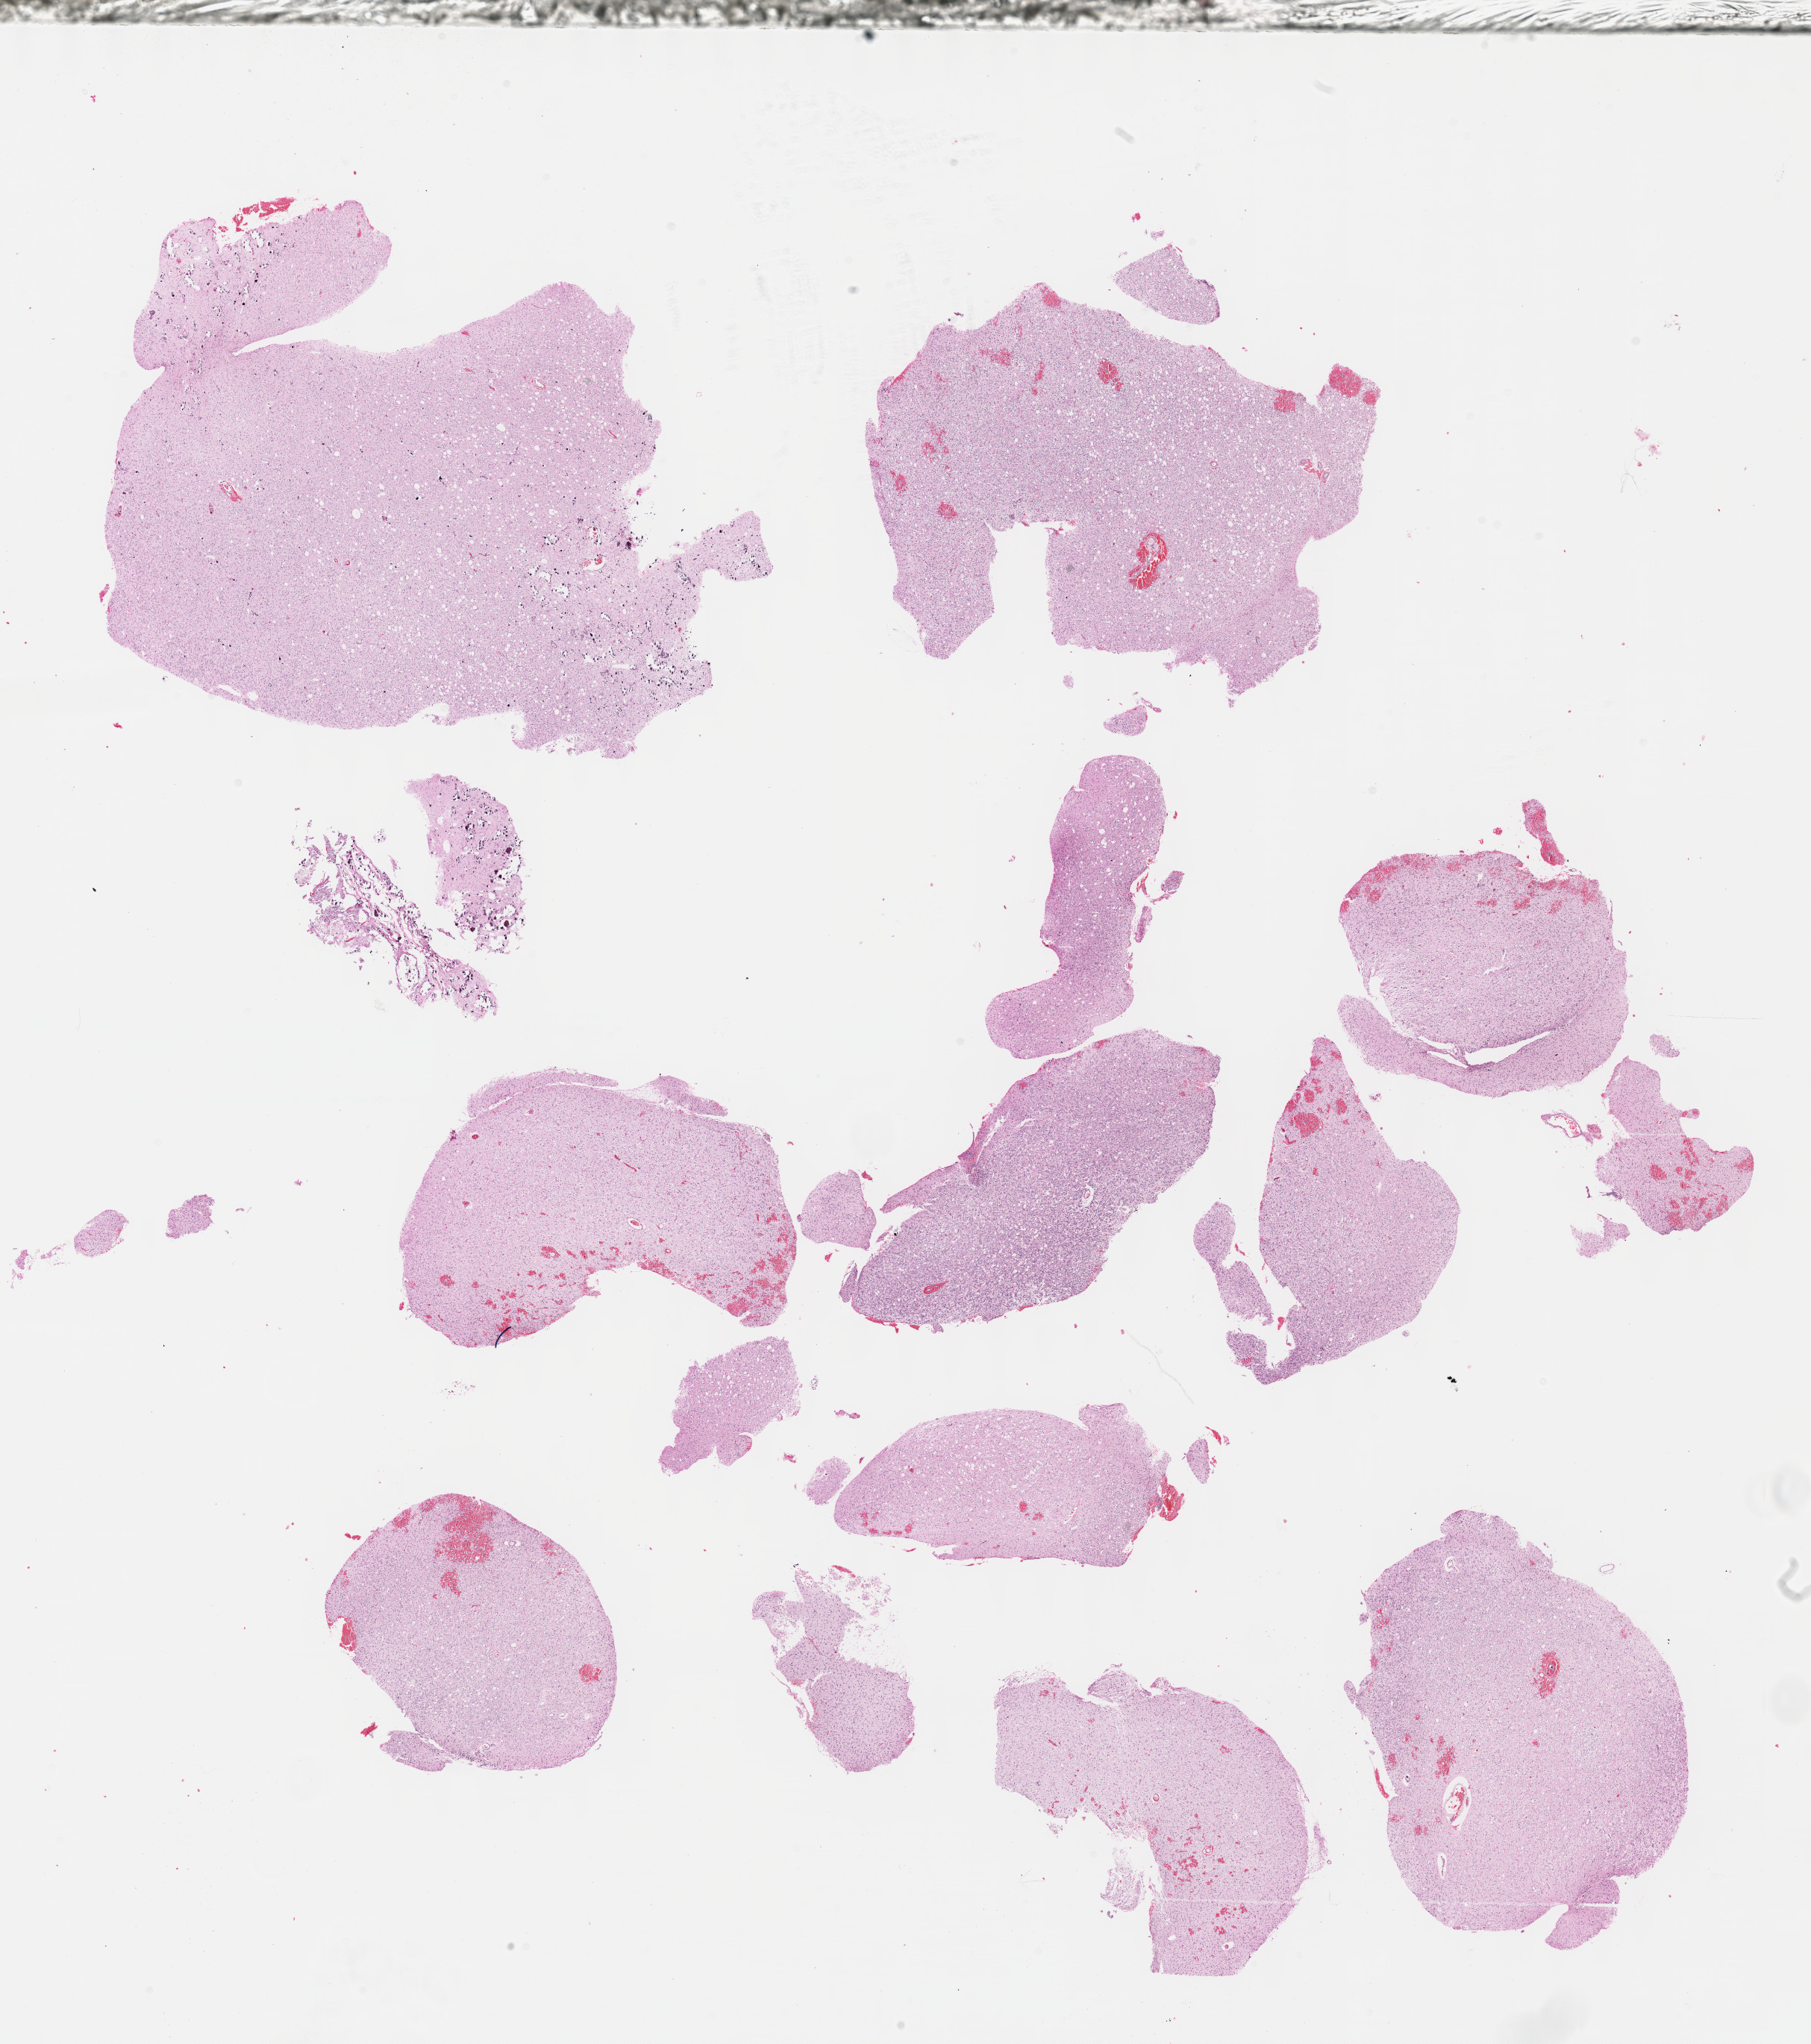
Digitized Hematoxylin and eosin (H&E) stained tissue section (whole slide), low-resolution overview of the scanned area, about 19.6 x 22.1 mm (slide scanned at 40x). Formalin-fixed paraffin-embedded (FFPE) diagnostic section. Brain, primary tumour sample. Patient: male, age at initial diagnosis 32 years. Histologic grade: G2 (moderately differentiated).
Pathologic diagnosis: Oligodendroglioma, NOS (cerebrum).